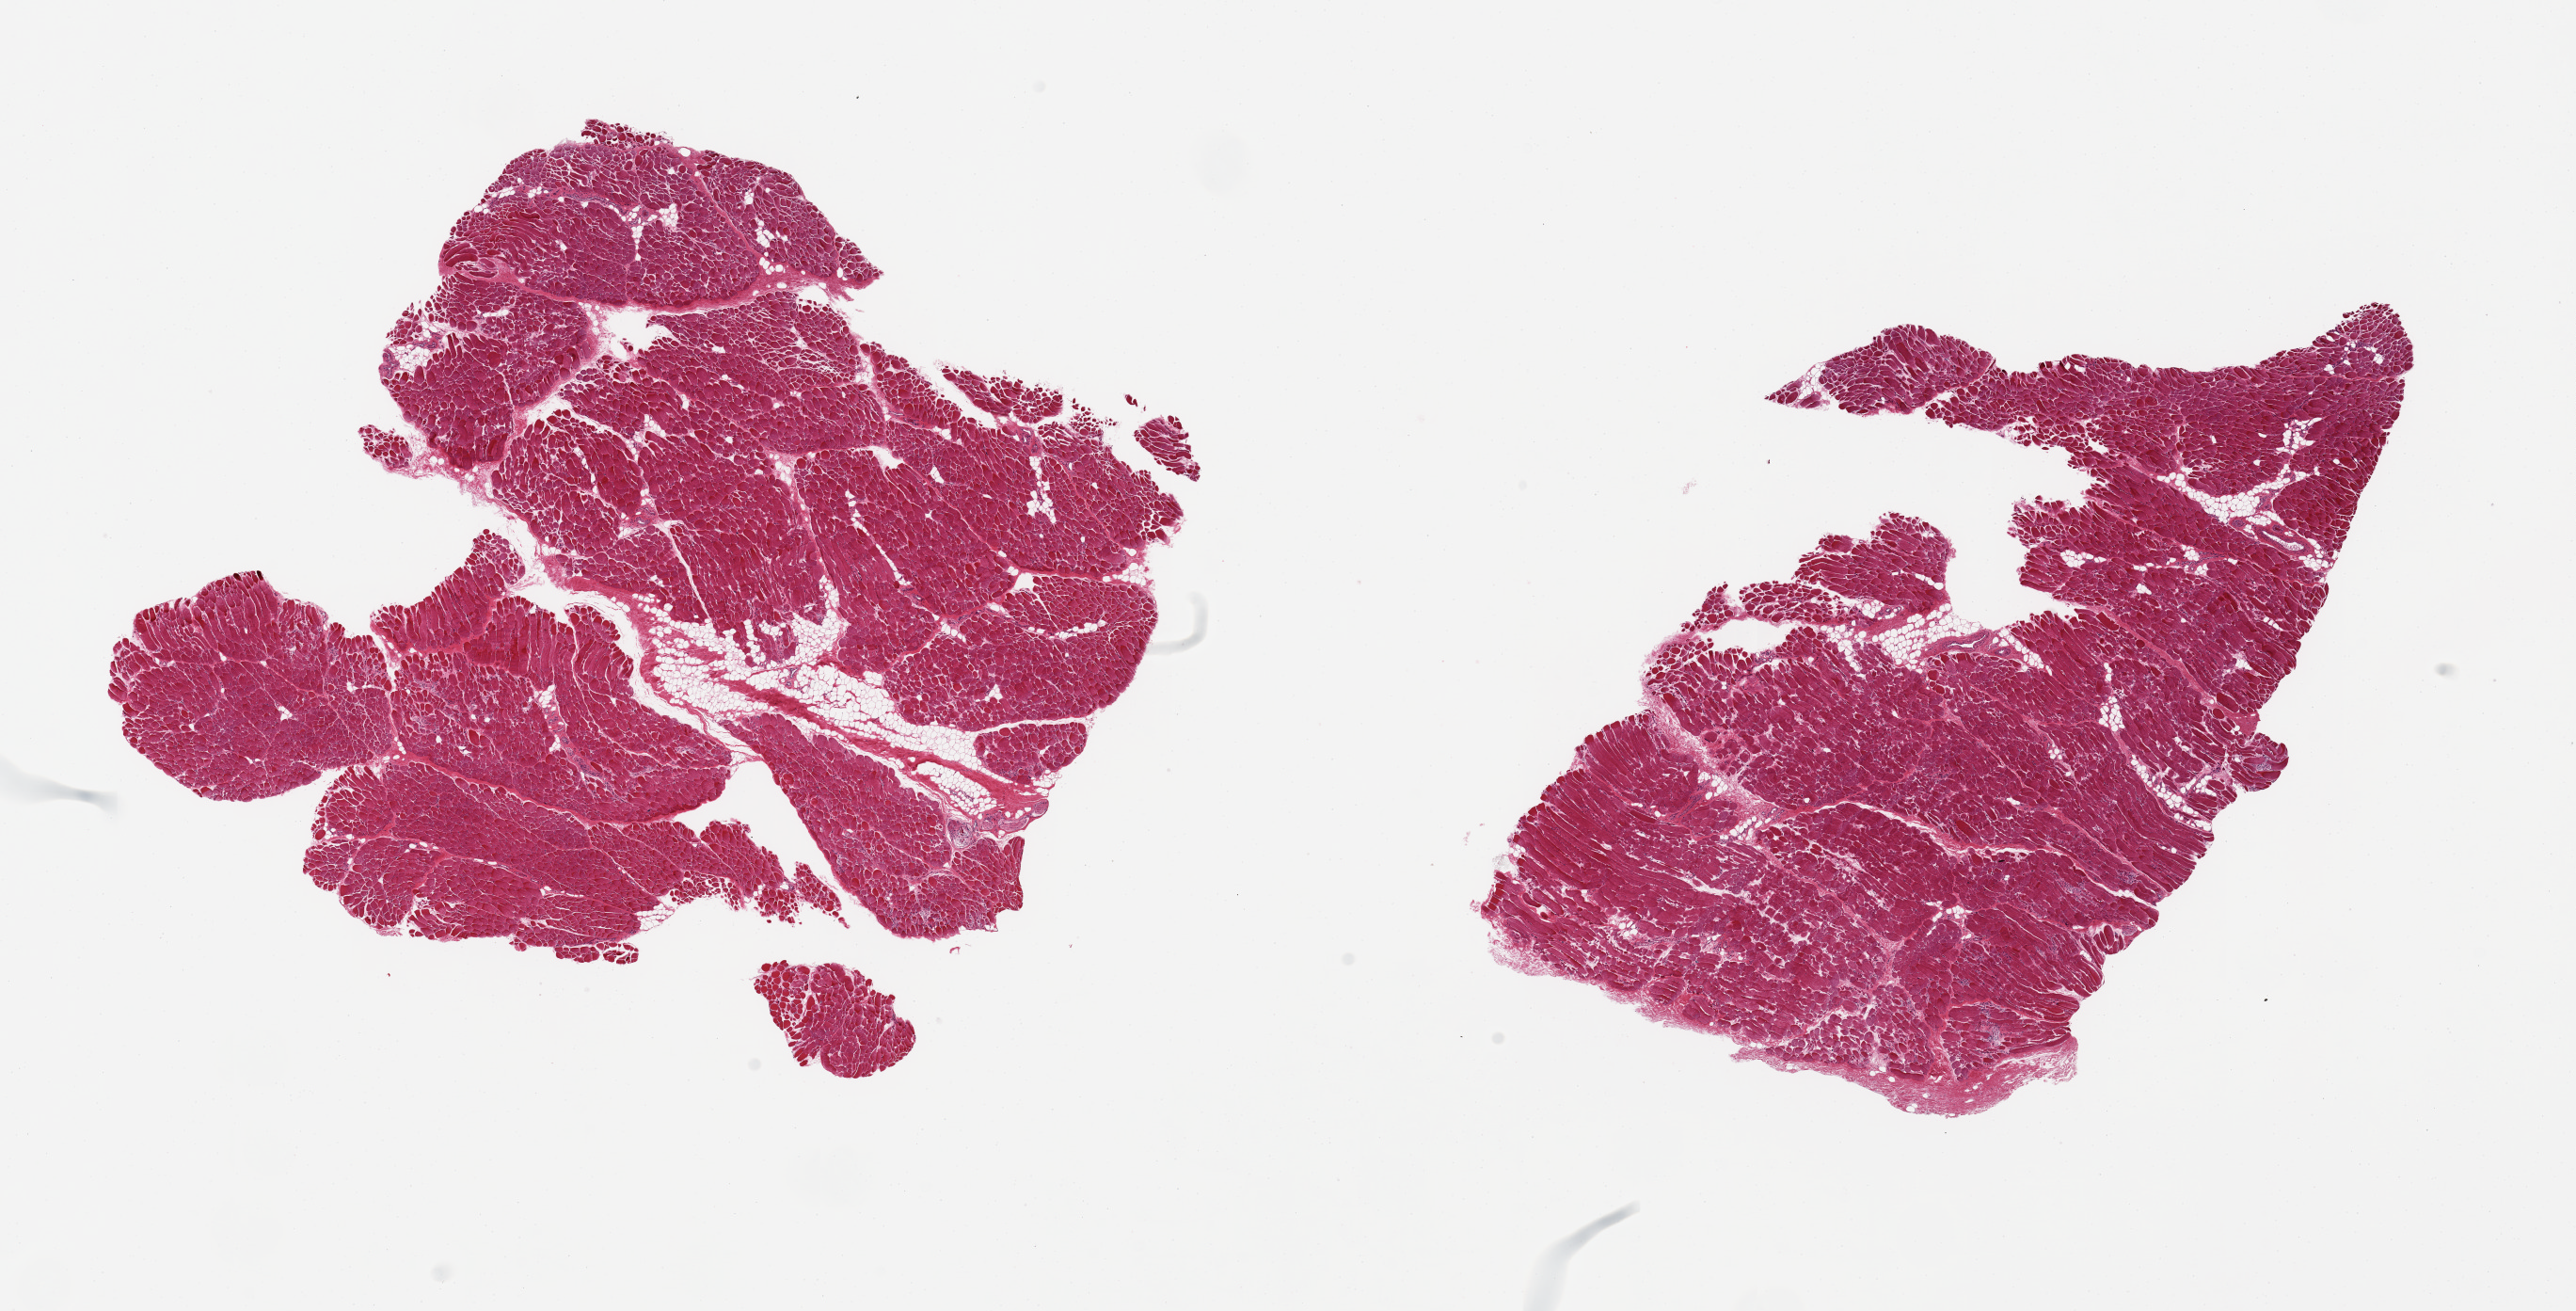
Digitized H&E-stained section, brightfield, low-resolution overview of the scanned area, about 21.7 x 11.0 mm; PAXgene-fixed, paraffin-embedded tissue; sampled site (target tissue): skeletal muscle; donor tissue sample. Female donor.
Review note (as recorded): 2 pieces, ~5-10% interstitital fat.